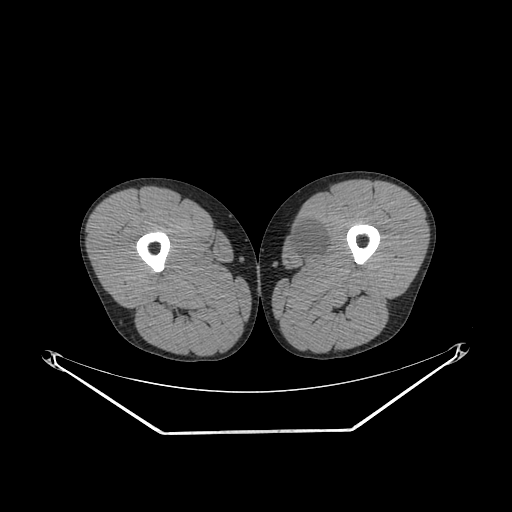
CT of an extremity soft-tissue mass (from a PET/CT study), one axial slice; slice 257 of 311 in the series (ordered by position); reconstruction kernel SOFT; 140 kVp; soft-tissue window (W 400 / L 40 HU); 3.75 mm slice thickness; 512 × 512 image matrix, field of view 500 × 500 mm. Male patient. From the clinical record (not read from this slice): histological type: mixoid liposarcoma; grade: low; site of the primary tumour: left thigh.
Annotated regions visible in this slice (expert contour drawn on MRI and transferred to this co-registered scan by the dataset authors):
- gross tumour volume (mass): bounding box [x1, y1, x2, y2] px = [288, 221, 328, 261]